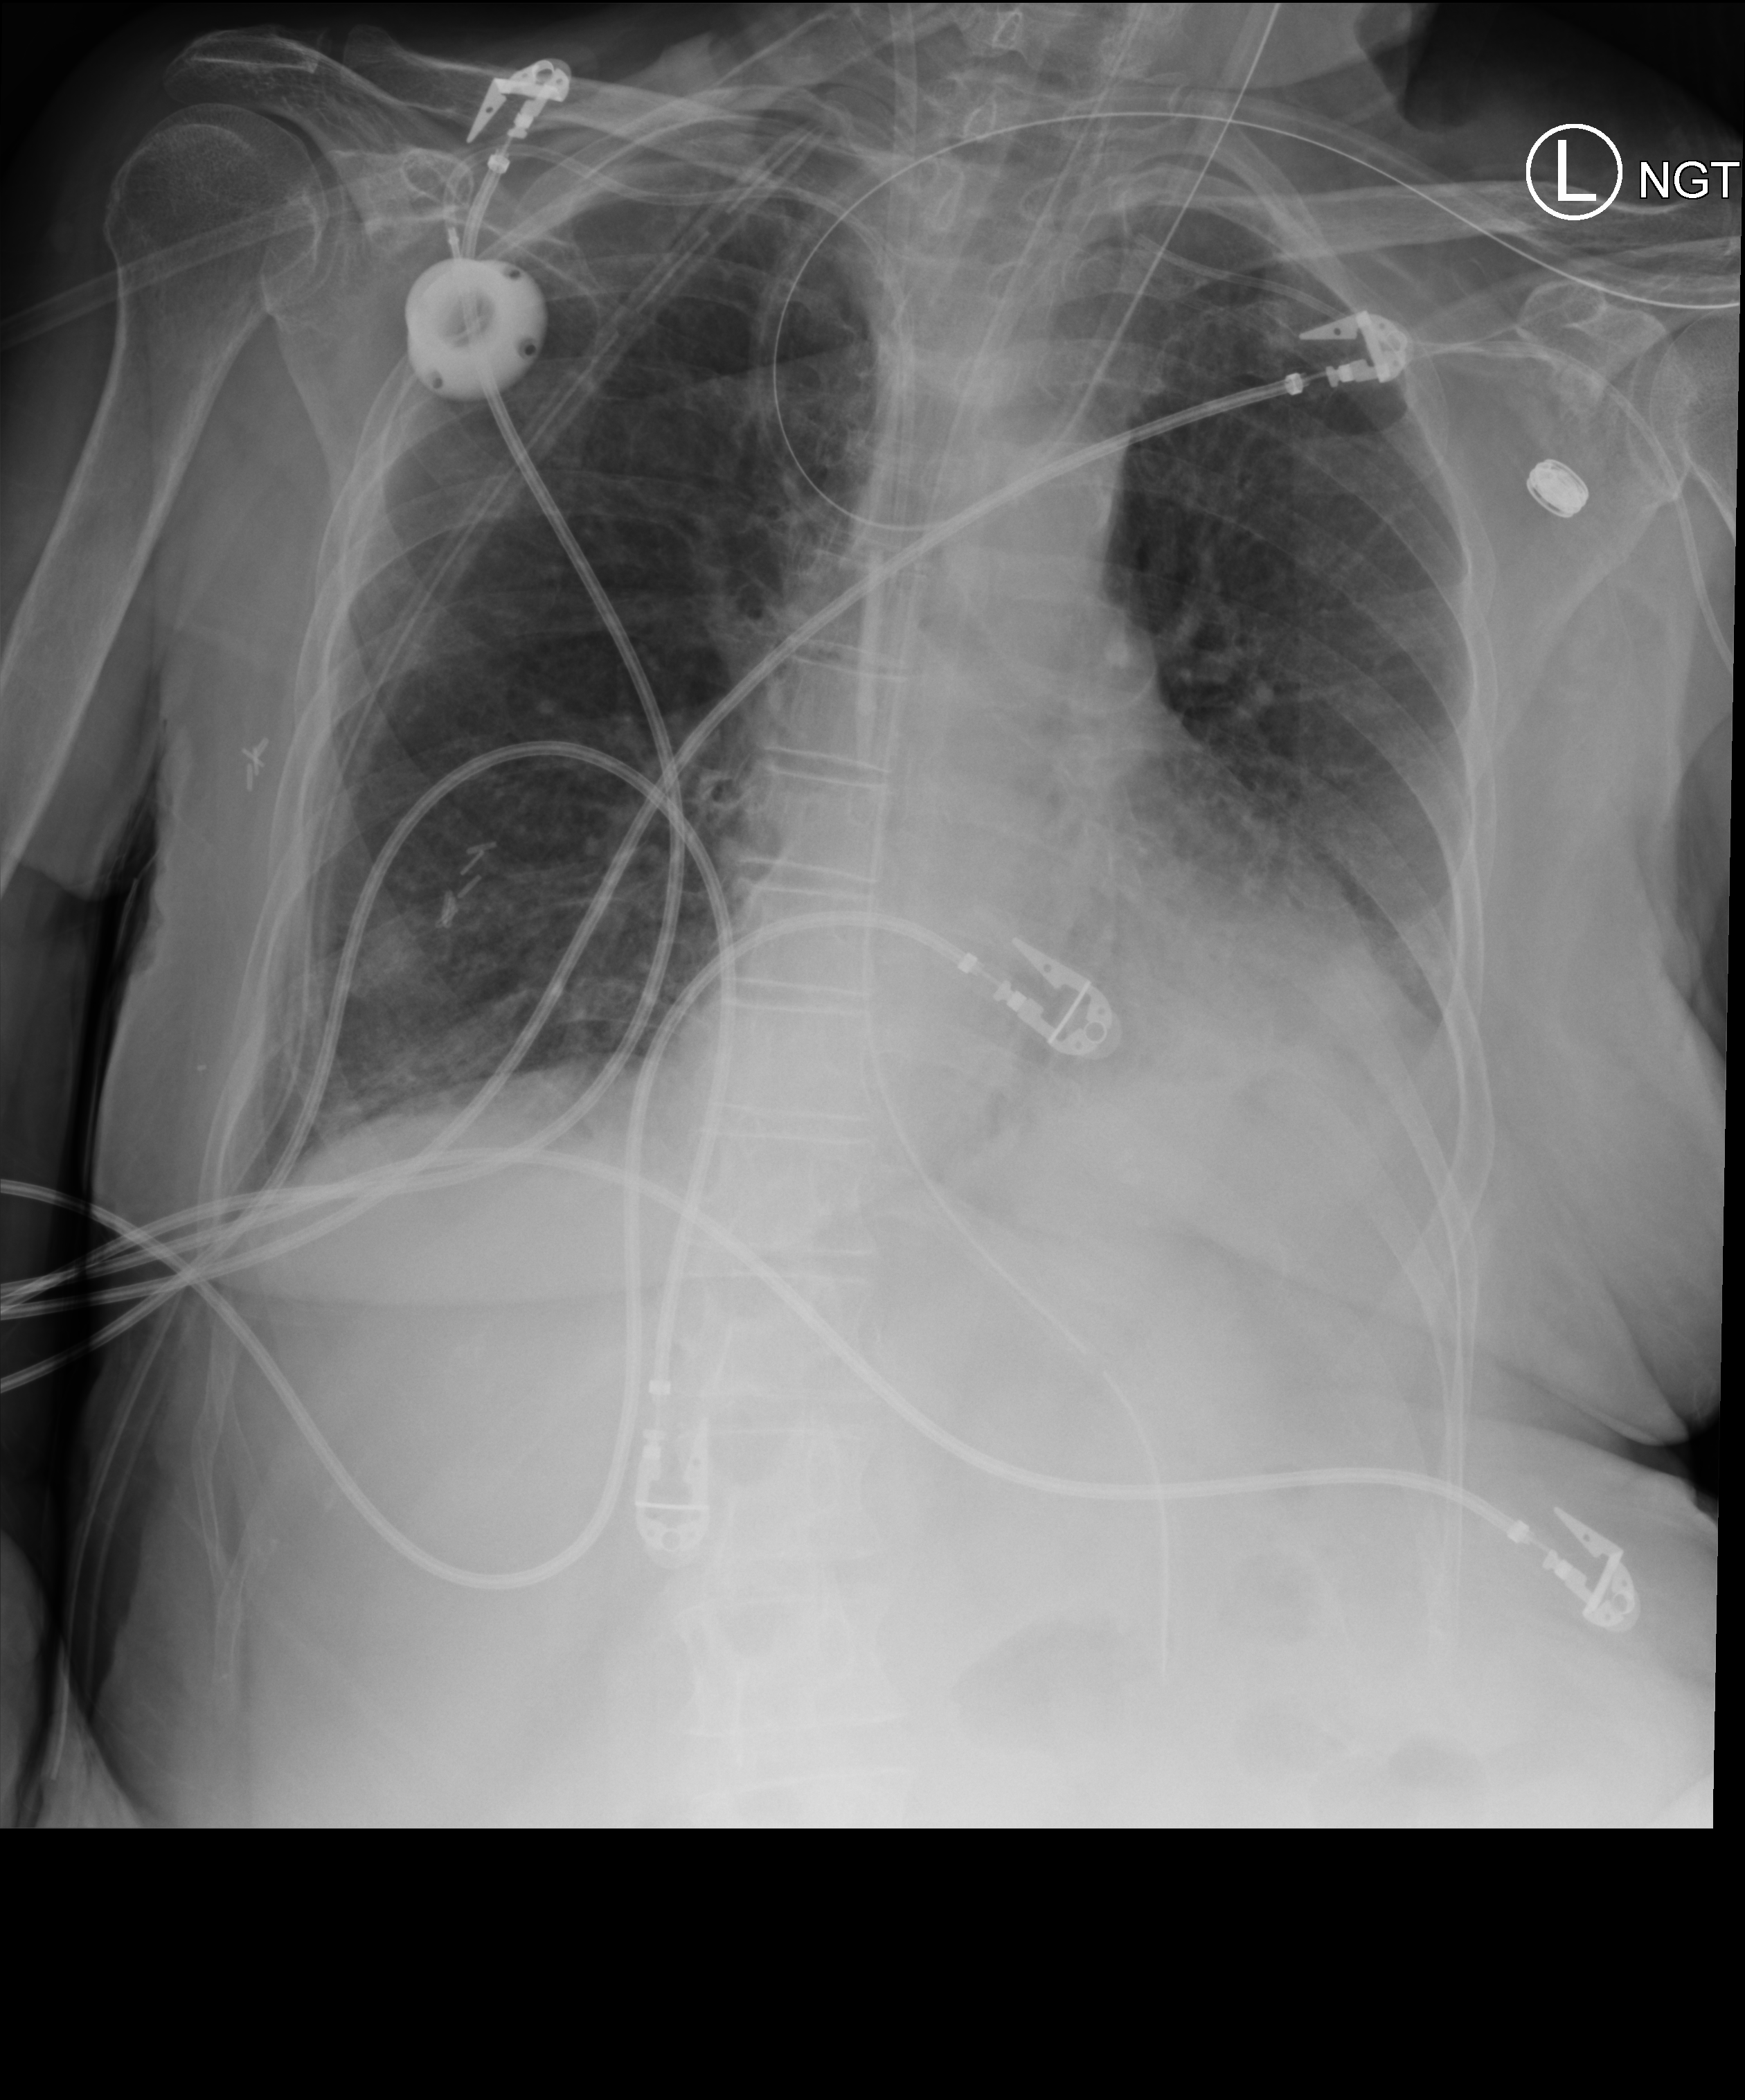
Bedside chest radiograph (computed radiography). Female patient hospitalised with COVID-19, age 60–74 years.
Hospital-stay facts (about this admission, not read from this image; timing relative to this image not recorded):
- mechanically ventilated during this hospital stay: yes
- admitted to intensive care during this hospital stay: yes
- length of hospital stay: 43 days